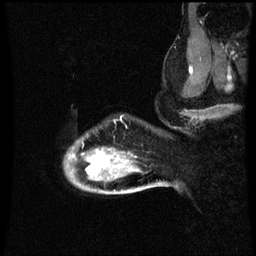
Breast MRI (dynamic contrast-enhanced), one sagittal slice. Dynamic contrast-enhanced series, image 2 of 3 at this slice position (ordered by acquisition). 1.5 T. TE 4.2 ms, TR 8.9 ms. 2 mm slice thickness. 256 × 256 image matrix, field of view 200 × 200 mm. Patient: female, 49 years. From the clinical record (not read from this slice): setting: breast cancer imaged before/during neoadjuvant chemotherapy; receptor status: HR-positive, HER2-negative.
Structures marked on this image (semi-automatically segmented with operator editing):
- analysis volume of interest (the breast-tissue region the enhancement analysis was run in; not a lesion): box from (x=66, y=134) to (x=159, y=195) px
- tumour enhancement mask (voxels above the 70 % enhancement threshold inside the analysis volume of interest): (x=86, y=150)–(x=123, y=175)